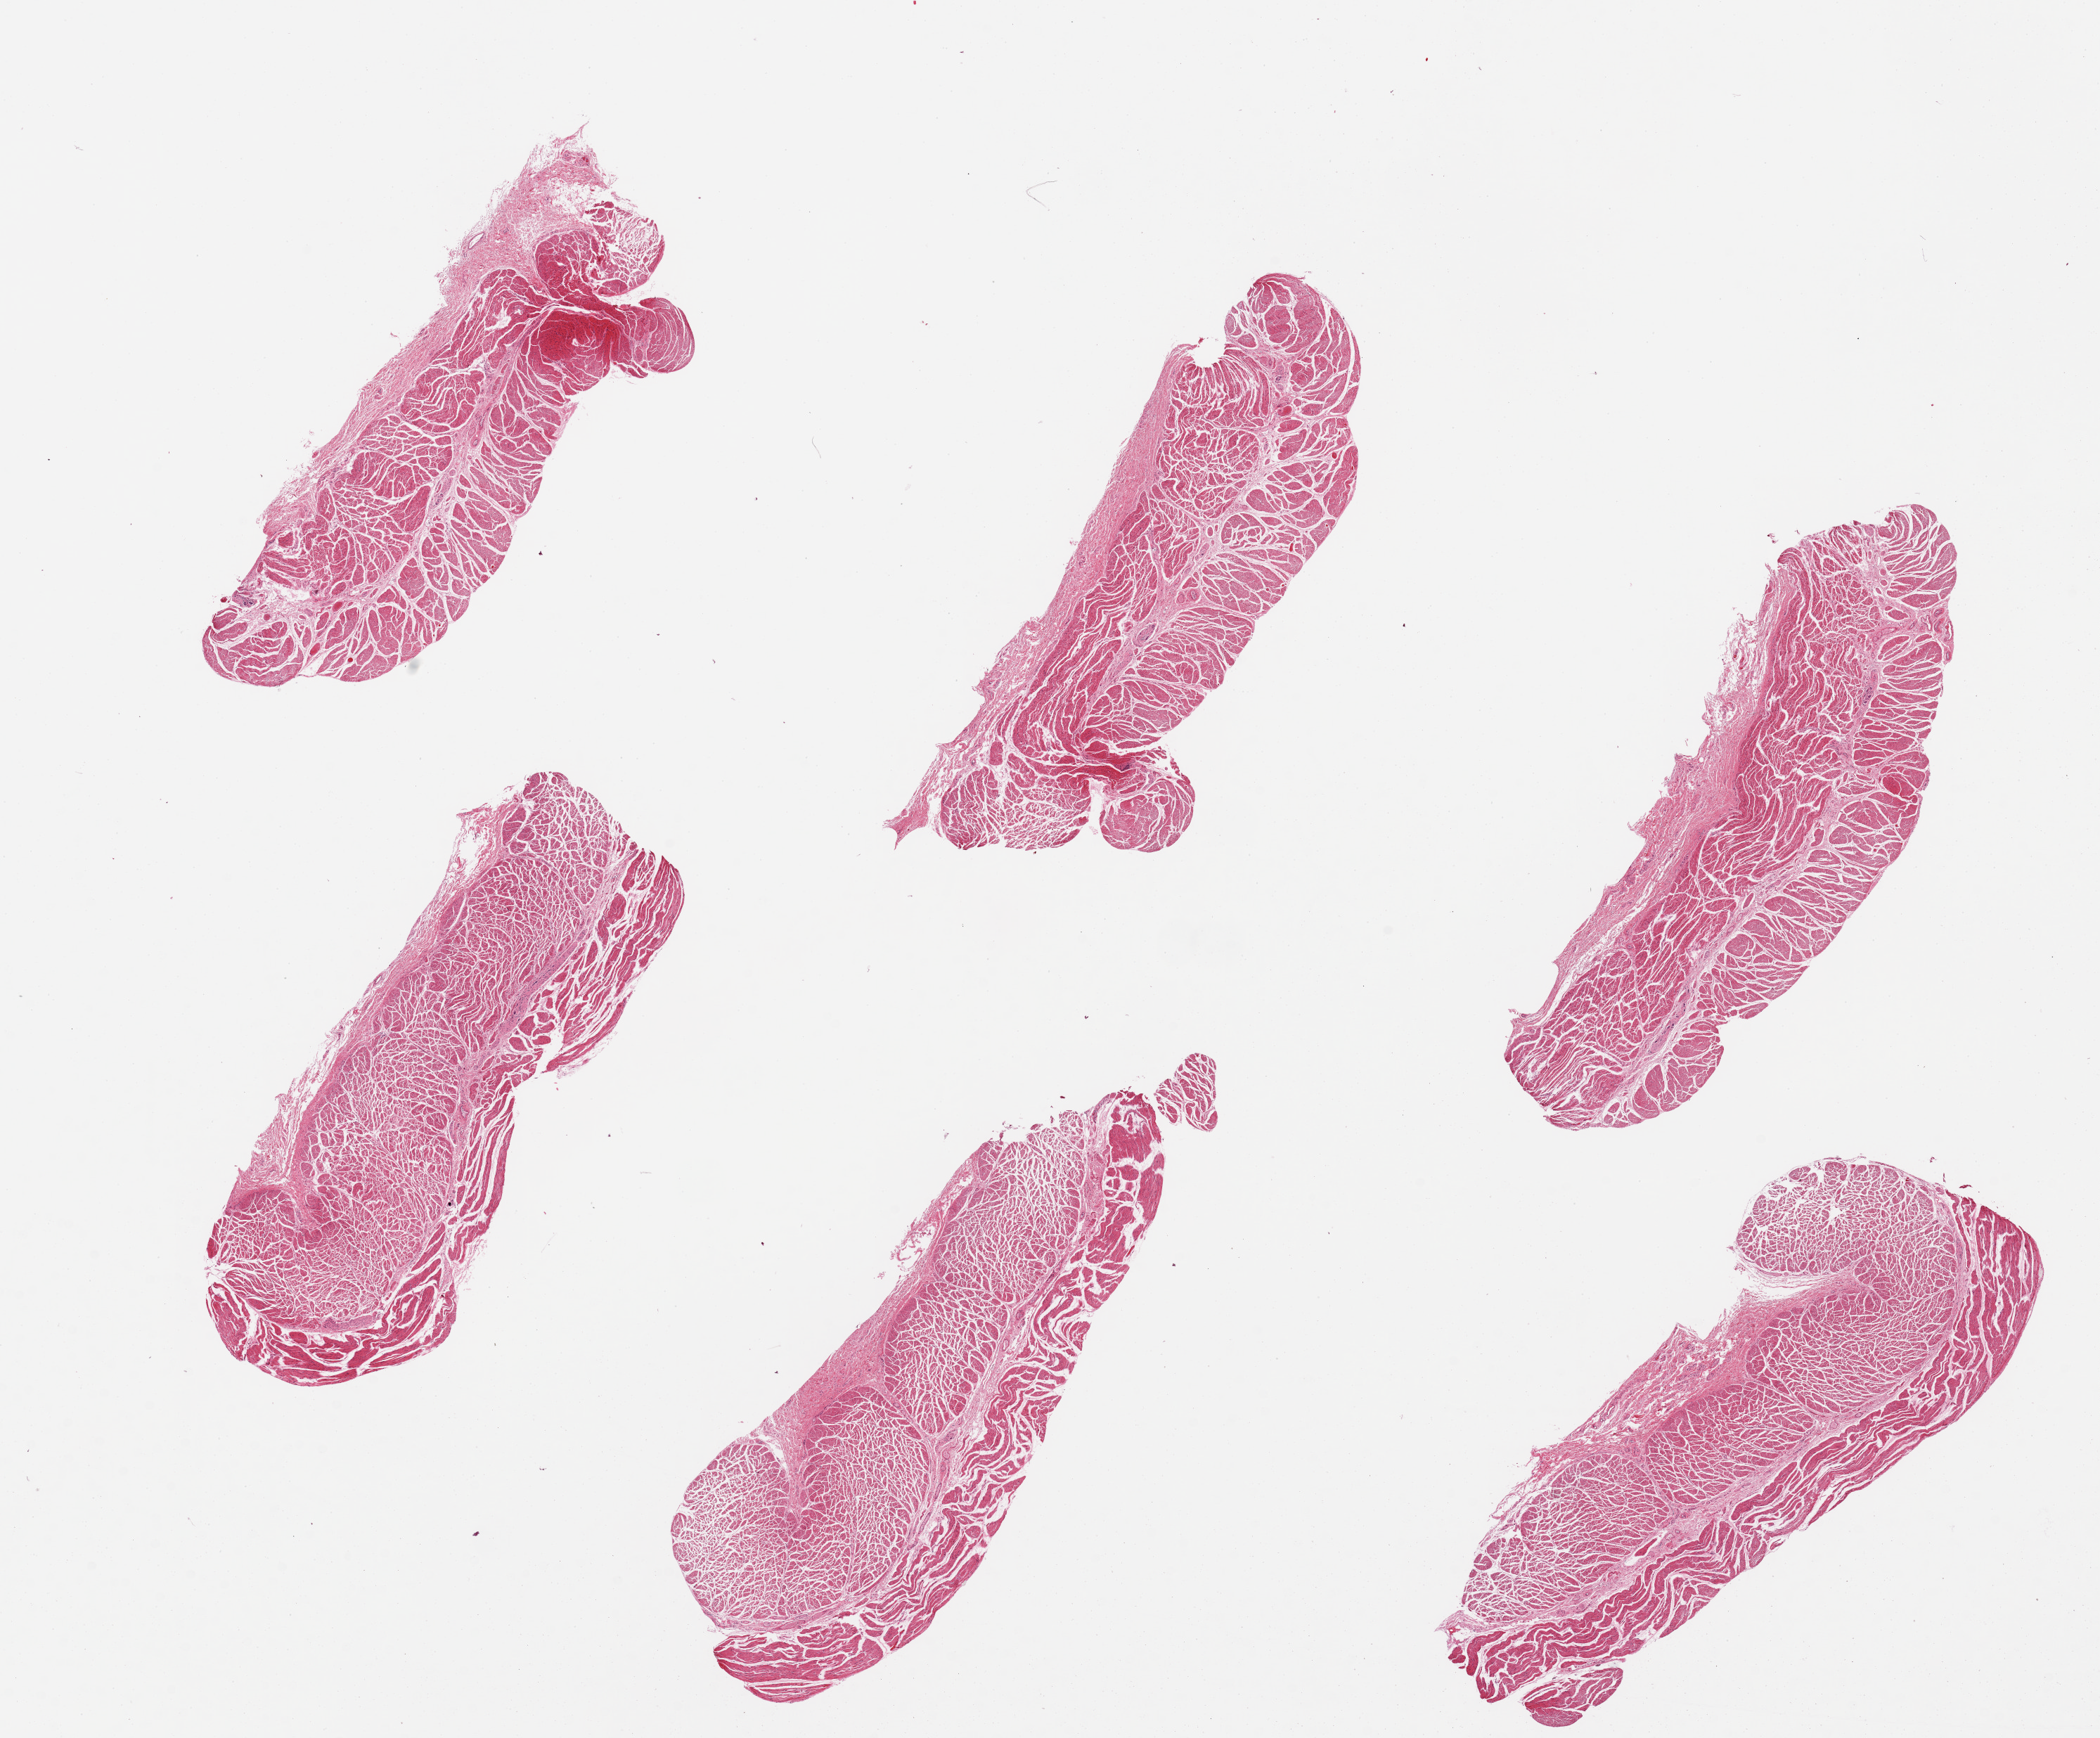
Haematoxylin and eosin whole-slide image — whole scanned area (about 23.6 x 19.6 mm, acquisition: 20x scan) shown as a low-resolution overview, PAXgene-fixed paraffin-embedded (PFPE) section, section of esophageal muscle (target tissue), donor tissue sample. Donor sex: female.
* pathologist's review note for this sample: 6 pieces, all muscularis, good specimens